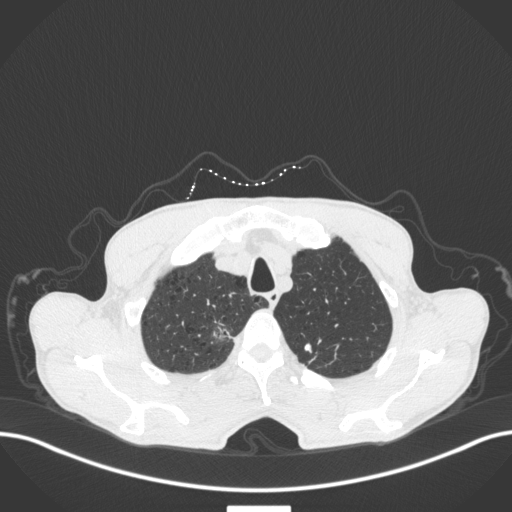
Chest CT, one axial slice; position 371 of 445 along the scan axis; reconstruction kernel B31f; lung window (W 1500 / L -600 HU); 1 mm slice thickness; 512 × 512 image matrix, field of view 400 × 400 mm. Patient: male, 70 years. Case-level facts recorded for this patient, not image findings: clinical TNM (as recorded): T1a N0 M0; histopathological grade: G1-2.
Structures marked on this image (bounding box drawn by a radiologist):
- lung tumour (recorded histology: adenocarcinoma): box from (x=208, y=314) to (x=234, y=343) px